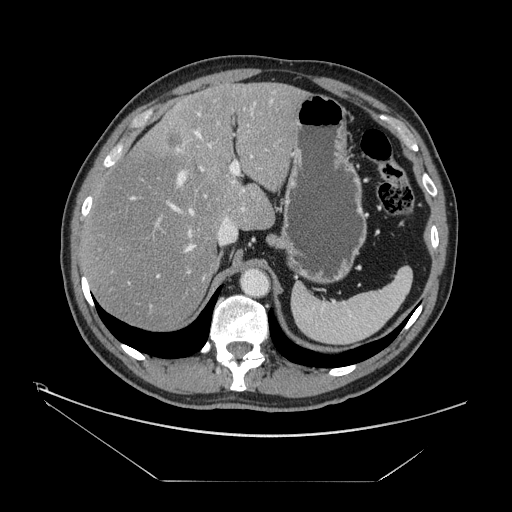
Contrast-enhanced abdominal CT, one axial slice; position 106 of 161 along the scan axis; intravenous contrast given; soft-tissue window (W 400 / L 40 HU); 2.5 mm slice thickness; 512 × 512 image matrix. Male patient, age 65 years. From the clinical record (not read from this slice): diagnosis: colorectal cancer liver metastases, imaged before liver resection; multiple liver metastases: yes; largest metastasis: 4.2 cm; chemotherapy before resection: yes.
Outlined on this slice (outlined manually by an expert reader):
- hepatic veins: bounding box [x1, y1, x2, y2] px = [128, 131, 211, 284]
- liver: [83, 83, 303, 330]
- planned liver remnant (the part of the liver to remain after resection): [83, 83, 302, 329]
- portal vein (with intrahepatic branches): [111, 91, 276, 311]
- liver metastasis: [169, 136, 183, 148]